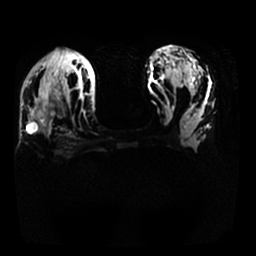
Breast MRI, one axial slice; position 17 of 25 along the scan axis; diffusion-weighted series; image 2 of 4 stored at this slice position (different b-values; order by instance number); 1.5 T; 4 mm slice thickness; 256 × 256 image matrix, field of view 340 × 340 mm. Female patient.
Structures marked on this image (manually delineated by an expert):
- tumour on diffusion-weighted imaging: bounding box (x1, y1, x2, y2) in pixels: (27, 98, 54, 128)